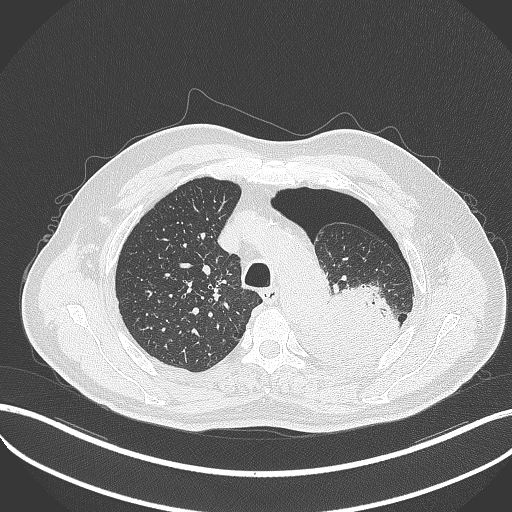
Chest CT, one axial slice. Lung window (W 1500 / L -600 HU). 1 mm slice thickness. 512 × 512 image matrix. Patient: male, 76 years. Case-level facts recorded for this patient, not image findings: clinical TNM (as recorded): T3 N0 M1b.
Structures marked on this image (bounding box drawn by a radiologist):
- lung tumour (recorded histology: adenocarcinoma): bounding box <299,282,404,371> (left, top, right, bottom; pixels)